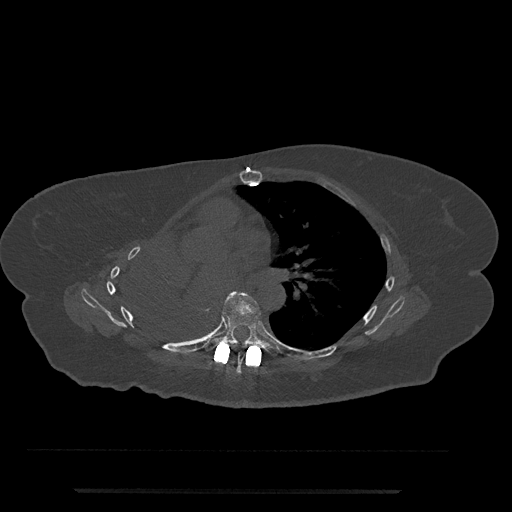
CT including the spine, one axial slice. Position 462 of 797 along the scan axis. Reconstruction kernel Br40s/3. 120 kVp. Bone window (W 1800 / L 400 HU). 0.5 mm slice thickness. 512 × 512 image matrix. Female patient, age 51 years. From the clinical record (not read from this slice): primary cancer: neuro; vertebrae with lytic lesions (as recorded): T8.
Structures marked on this image (semi-automatically segmented with operator editing):
- T6 vertebra: bounding box <227,353,245,373> (left, top, right, bottom; pixels)
- T7 vertebra: <193,292,279,357>